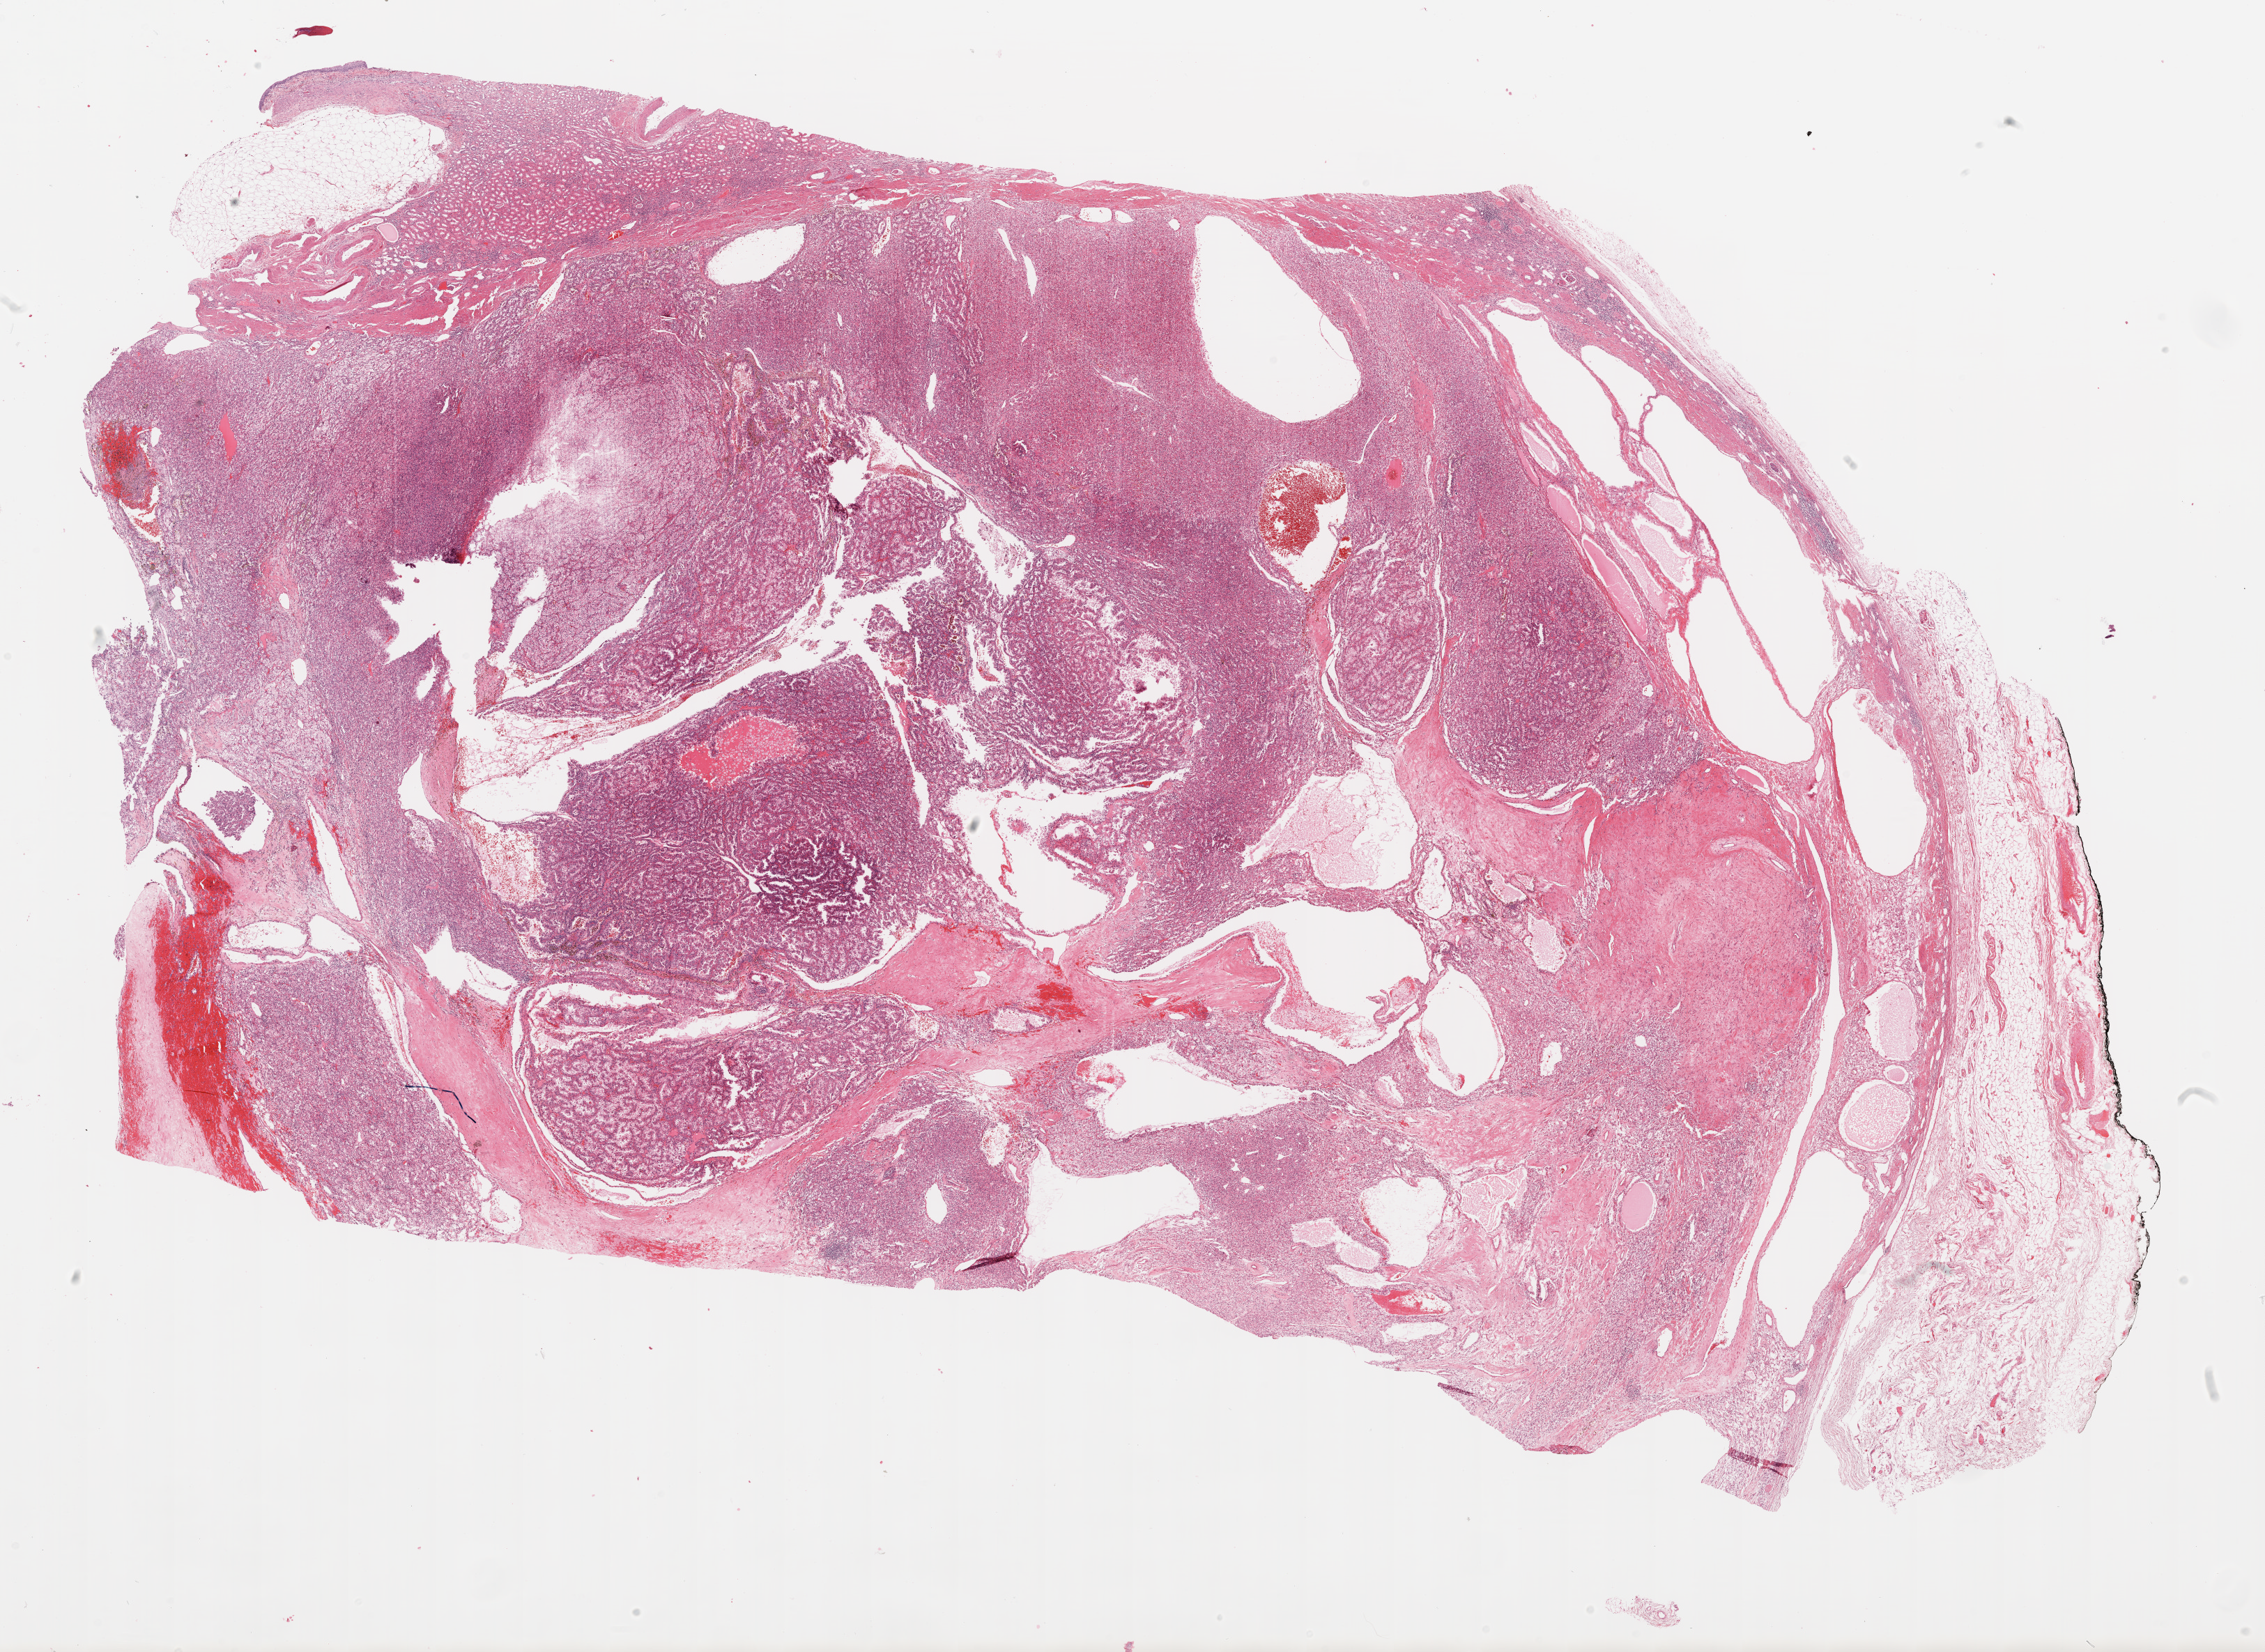
Whole-slide histology image, H&E — whole scanned area (about 26.1 x 19.0 mm, slide scanned at 20x) shown as a low-resolution overview, formalin-fixed paraffin-embedded (FFPE) diagnostic section, kidney, primary tumour sample. Female patient; age at initial diagnosis 79 years.
Histologic diagnosis: Clear cell adenocarcinoma, NOS.